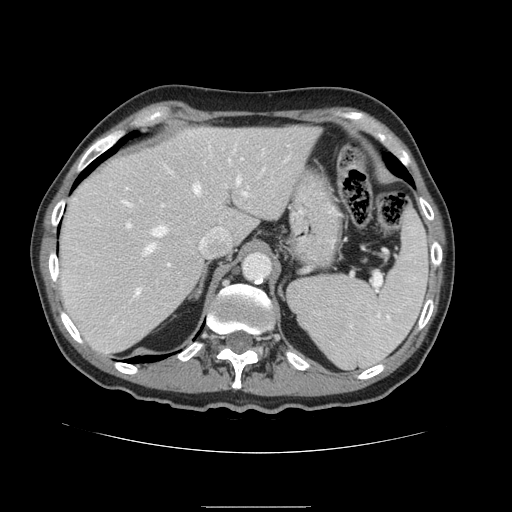
Contrast-enhanced abdominal CT, one axial slice. 120 kVp. Intravenous contrast given. Soft-tissue window (W 400 / L 40 HU). 2.5 mm slice thickness. 512 × 512 image matrix, field of view 386 × 386 mm. Male patient, age 74 years. From the clinical record (not read from this slice): diagnosis: colorectal cancer liver metastases, imaged before liver resection; multiple liver metastases: no; largest metastasis: 14.5 cm; disease in both lobes: yes.
Outlined on this slice (outlined manually by an expert reader):
- hepatic veins: bounding box [x1, y1, x2, y2] px = [126, 178, 241, 252]
- liver: [59, 126, 320, 354]
- planned liver remnant (the part of the liver to remain after resection): [60, 127, 320, 354]
- portal vein (with intrahepatic branches): [94, 191, 249, 297]